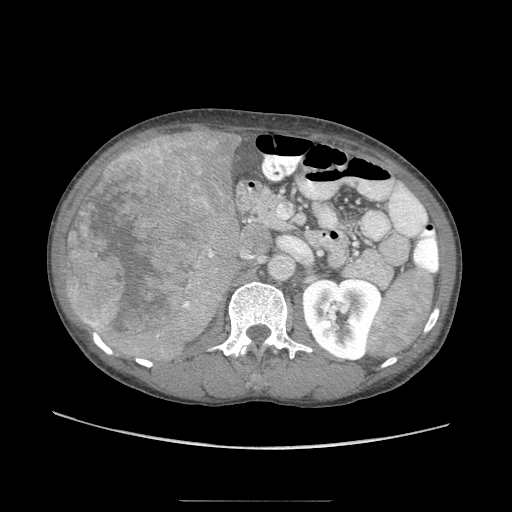
Contrast-enhanced abdominal CT (liver protocol), one axial slice; position 36 of 103 along the scan axis; reconstruction kernel STANDARD; soft-tissue window (W 400 / L 40 HU); 512 × 512 image matrix, field of view 380 × 380 mm. From the clinical record (not read from this slice): diagnosis: hepatocellular carcinoma (patient treated with transarterial chemoembolisation; whether this scan precedes or follows treatment is not stated here); TNM stage (as recorded): Stage-IIIA; Child-Pugh class: A; tumour differentiation: moderately differentiated.
Outlined on this slice (semi-automatically segmented with operator editing):
- liver parenchyma outside the tumour (the mass and vessels are separate outlines, so this box may not span the whole liver): bounding box <64,126,240,354> (left, top, right, bottom; pixels)
- mass: <64,138,220,345>